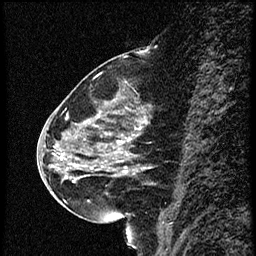
Breast MRI (dynamic contrast-enhanced), one sagittal slice; position 26 of 56 along the scan axis; dynamic contrast-enhanced study with each time point stored as its own series, time point 2 of 4 at this slice position (early post-contrast, ordered by acquisition time); 1.5 T; TE 4.2 ms, TR 18.9 ms; 2 mm slice thickness; 256 × 256 image matrix, field of view 200 × 200 mm. Female patient. Case-level facts recorded for this patient, not image findings: setting: breast cancer imaged before/during neoadjuvant chemotherapy; receptor status: HER2-positive.
Outlined on this slice (semi-automatically segmented with operator editing):
- analysis volume of interest (the breast-tissue region the enhancement analysis was run in; not a lesion): bounding box [x1, y1, x2, y2] px = [63, 80, 168, 215]
- tumour enhancement mask (voxels above the 100 % enhancement threshold inside the analysis volume of interest): [74, 142, 128, 183]